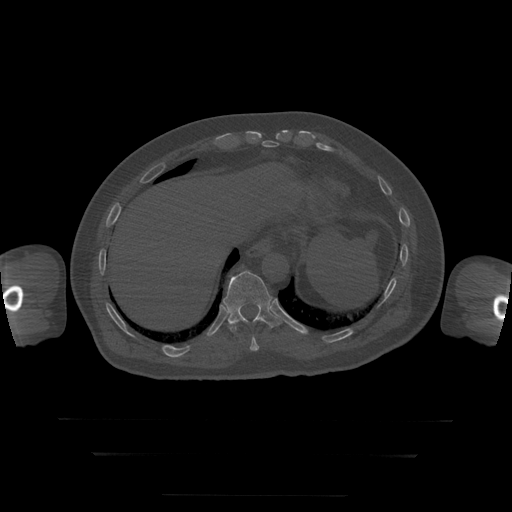
CT including the spine, one axial slice; position 107 of 397 along the scan axis; bone window (W 1800 / L 400 HU); 512 × 512 image matrix. Patient age 73 years. Case-level facts recorded for this patient, not image findings: primary cancer: prostate.
Outlined on this slice (semi-automatic segmentation, software-assisted and operator-edited):
- T10 vertebra: bounding box (x1, y1, x2, y2) in pixels: (250, 337, 260, 351)
- T11 vertebra: (223, 271, 282, 332)